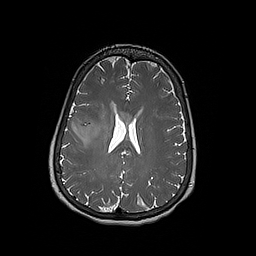
Brain MRI from a brain-tumour surgery series, one axial slice. Slice 80 of 192 in the series (ordered by position). 256 × 256 image matrix, field of view 250 × 250 mm. From the clinical record (not read from this slice): histopathology: Oligodendroglioma; WHO grade: 3; IDH mutation: yes; tumour location: Right Frontal.
Structures marked on this image (outlined manually by an expert reader):
- tumour: box from (x=72, y=115) to (x=100, y=141) px